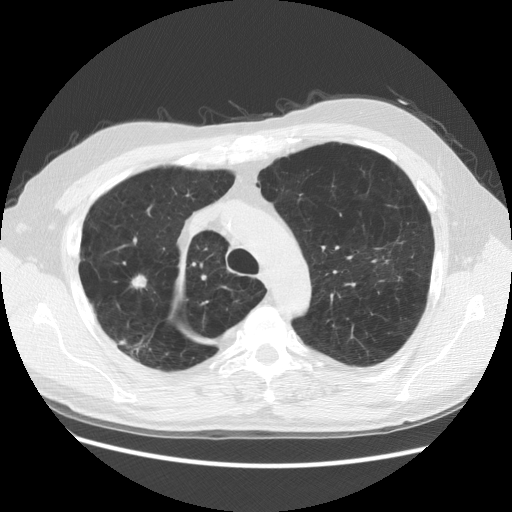
Low-dose screening chest CT, one axial slice; slice 103 of 137 in the series (ordered by position); 140 kVp; lung window (W 1500 / L -600 HU); 2.5 mm slice thickness; 512 × 512 image matrix, field of view 377 × 377 mm.
Outlined on this slice (expert manual segmentation):
- lesion 1 (tumor, upper lobe of right lung): box from (x=131, y=274) to (x=147, y=289) px